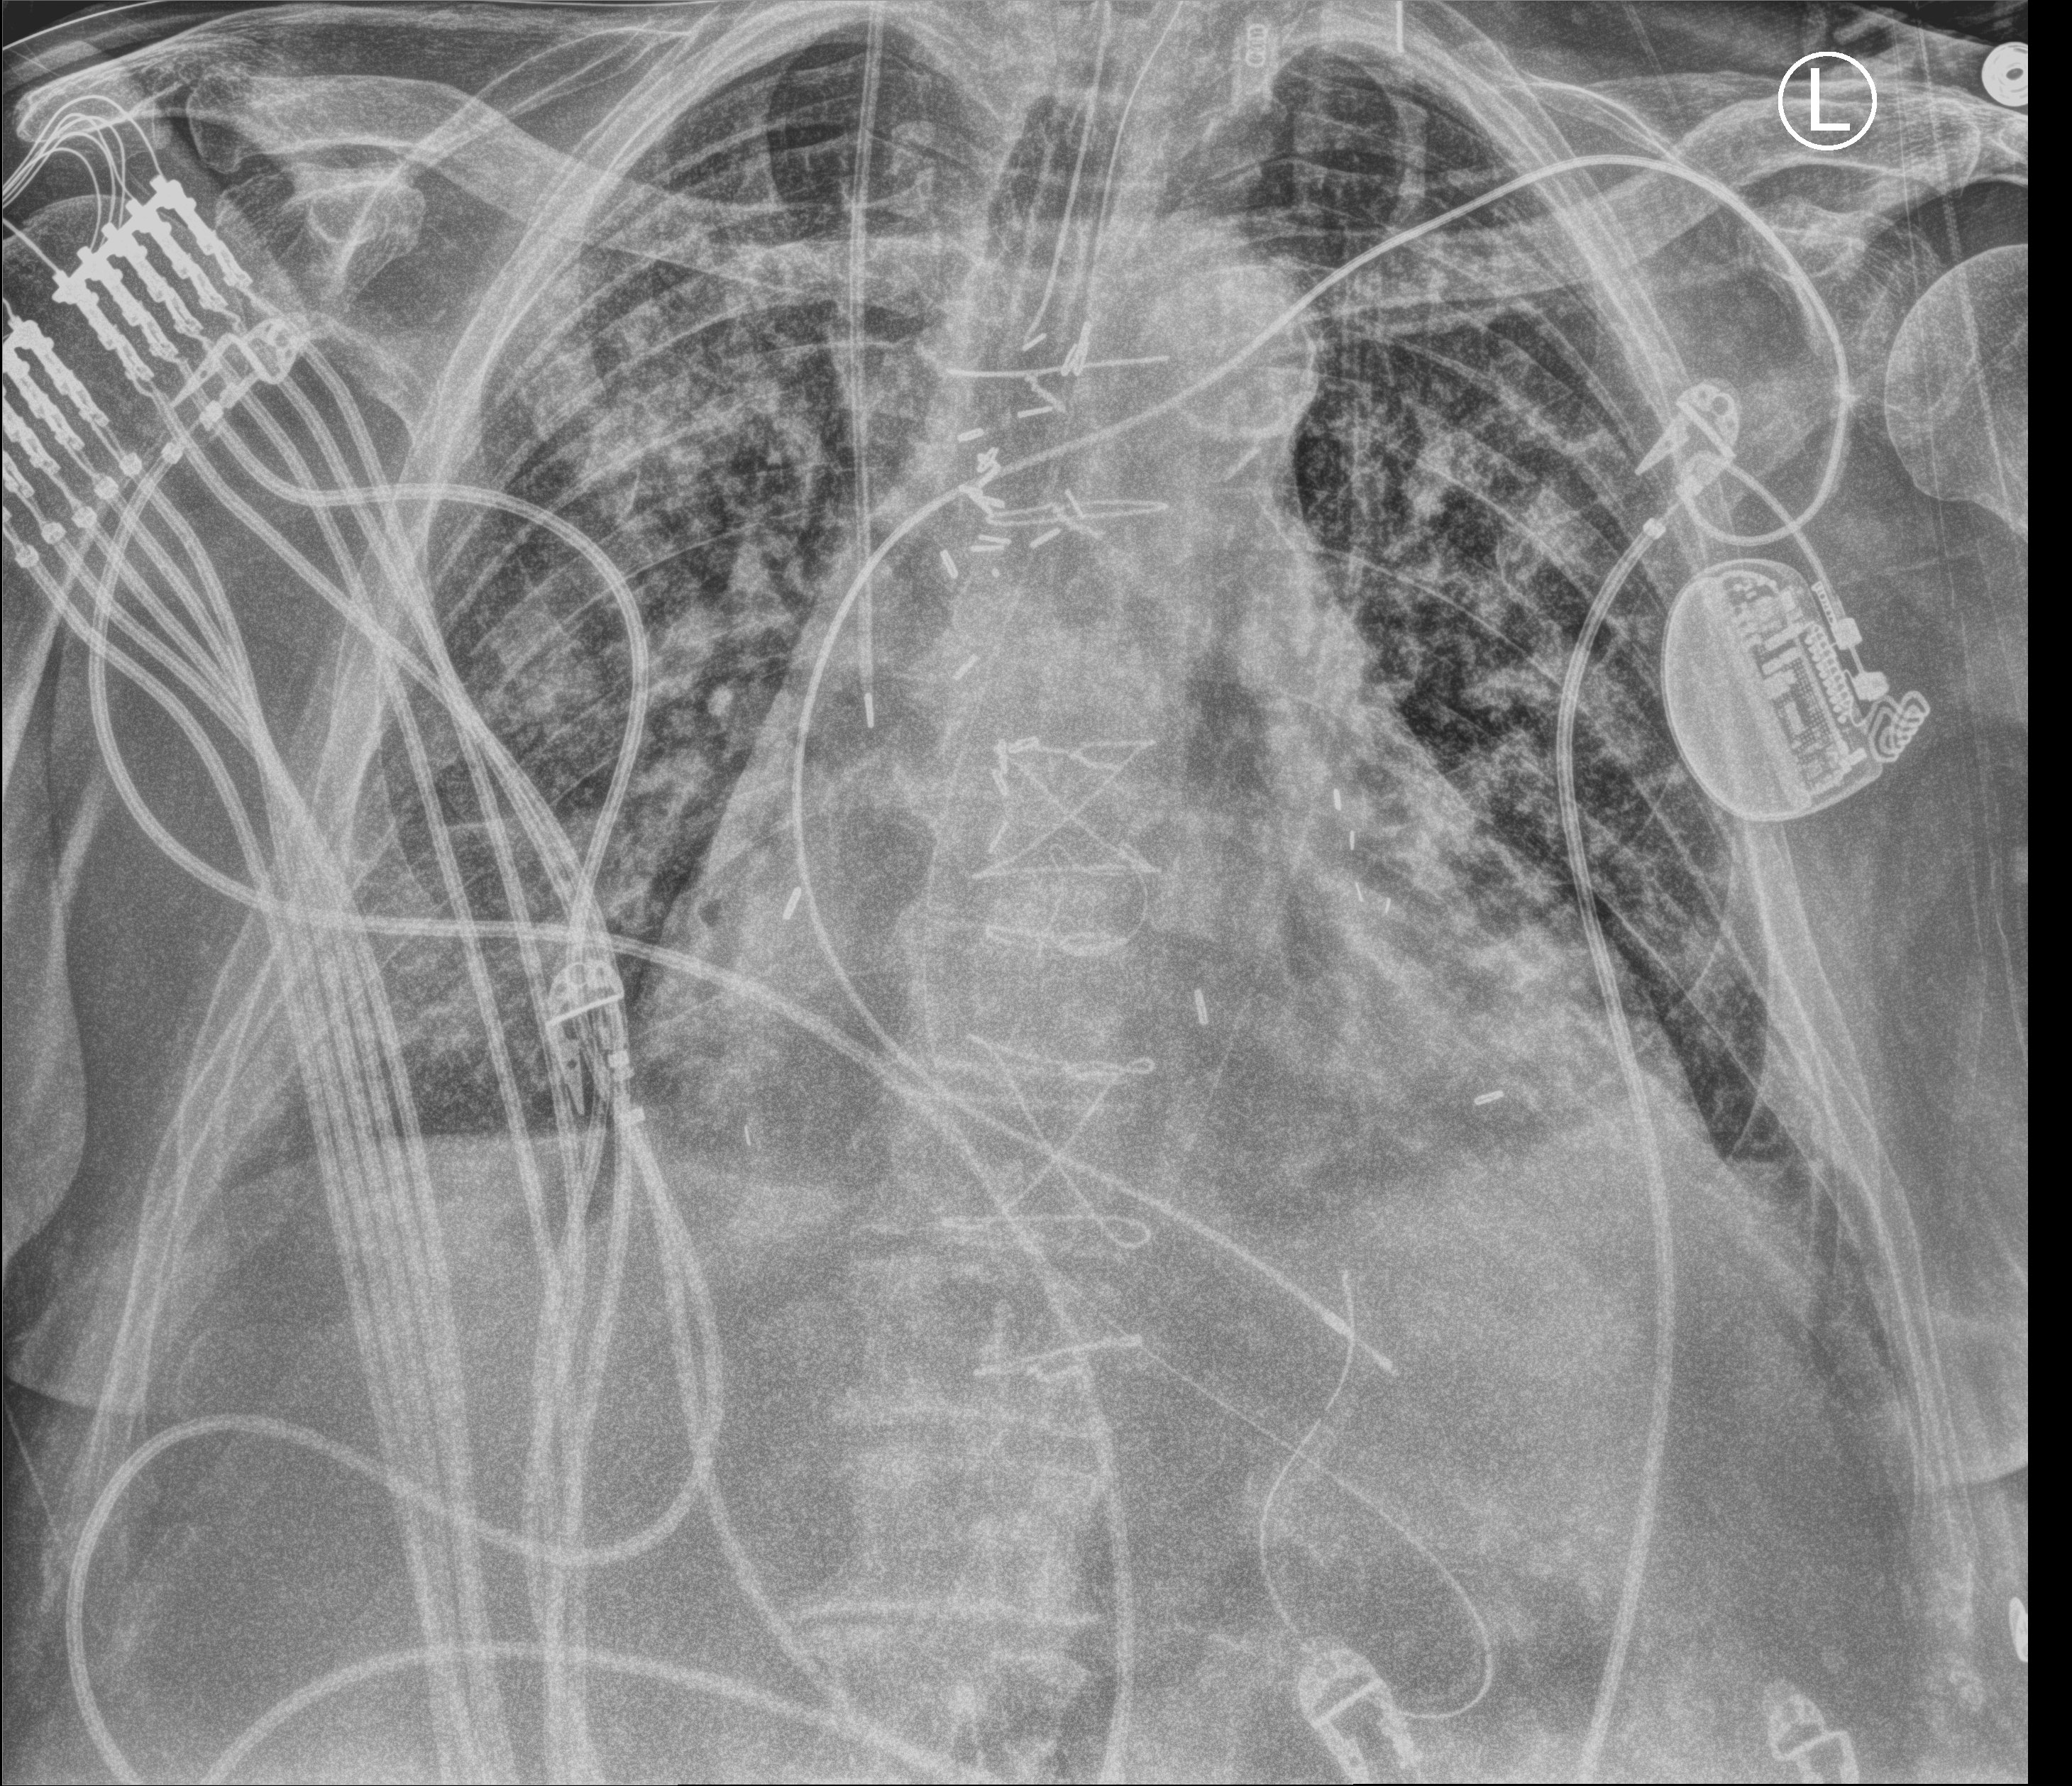
Portable chest radiograph; anteroposterior (AP) projection. Patient hospitalised with COVID-19; male, aged 75–90 years.
From the hospital-stay record, not from the radiograph (when in the stay this image was taken is not recorded): smoking status (admission record): former; admitted to intensive care during this hospital stay: yes.